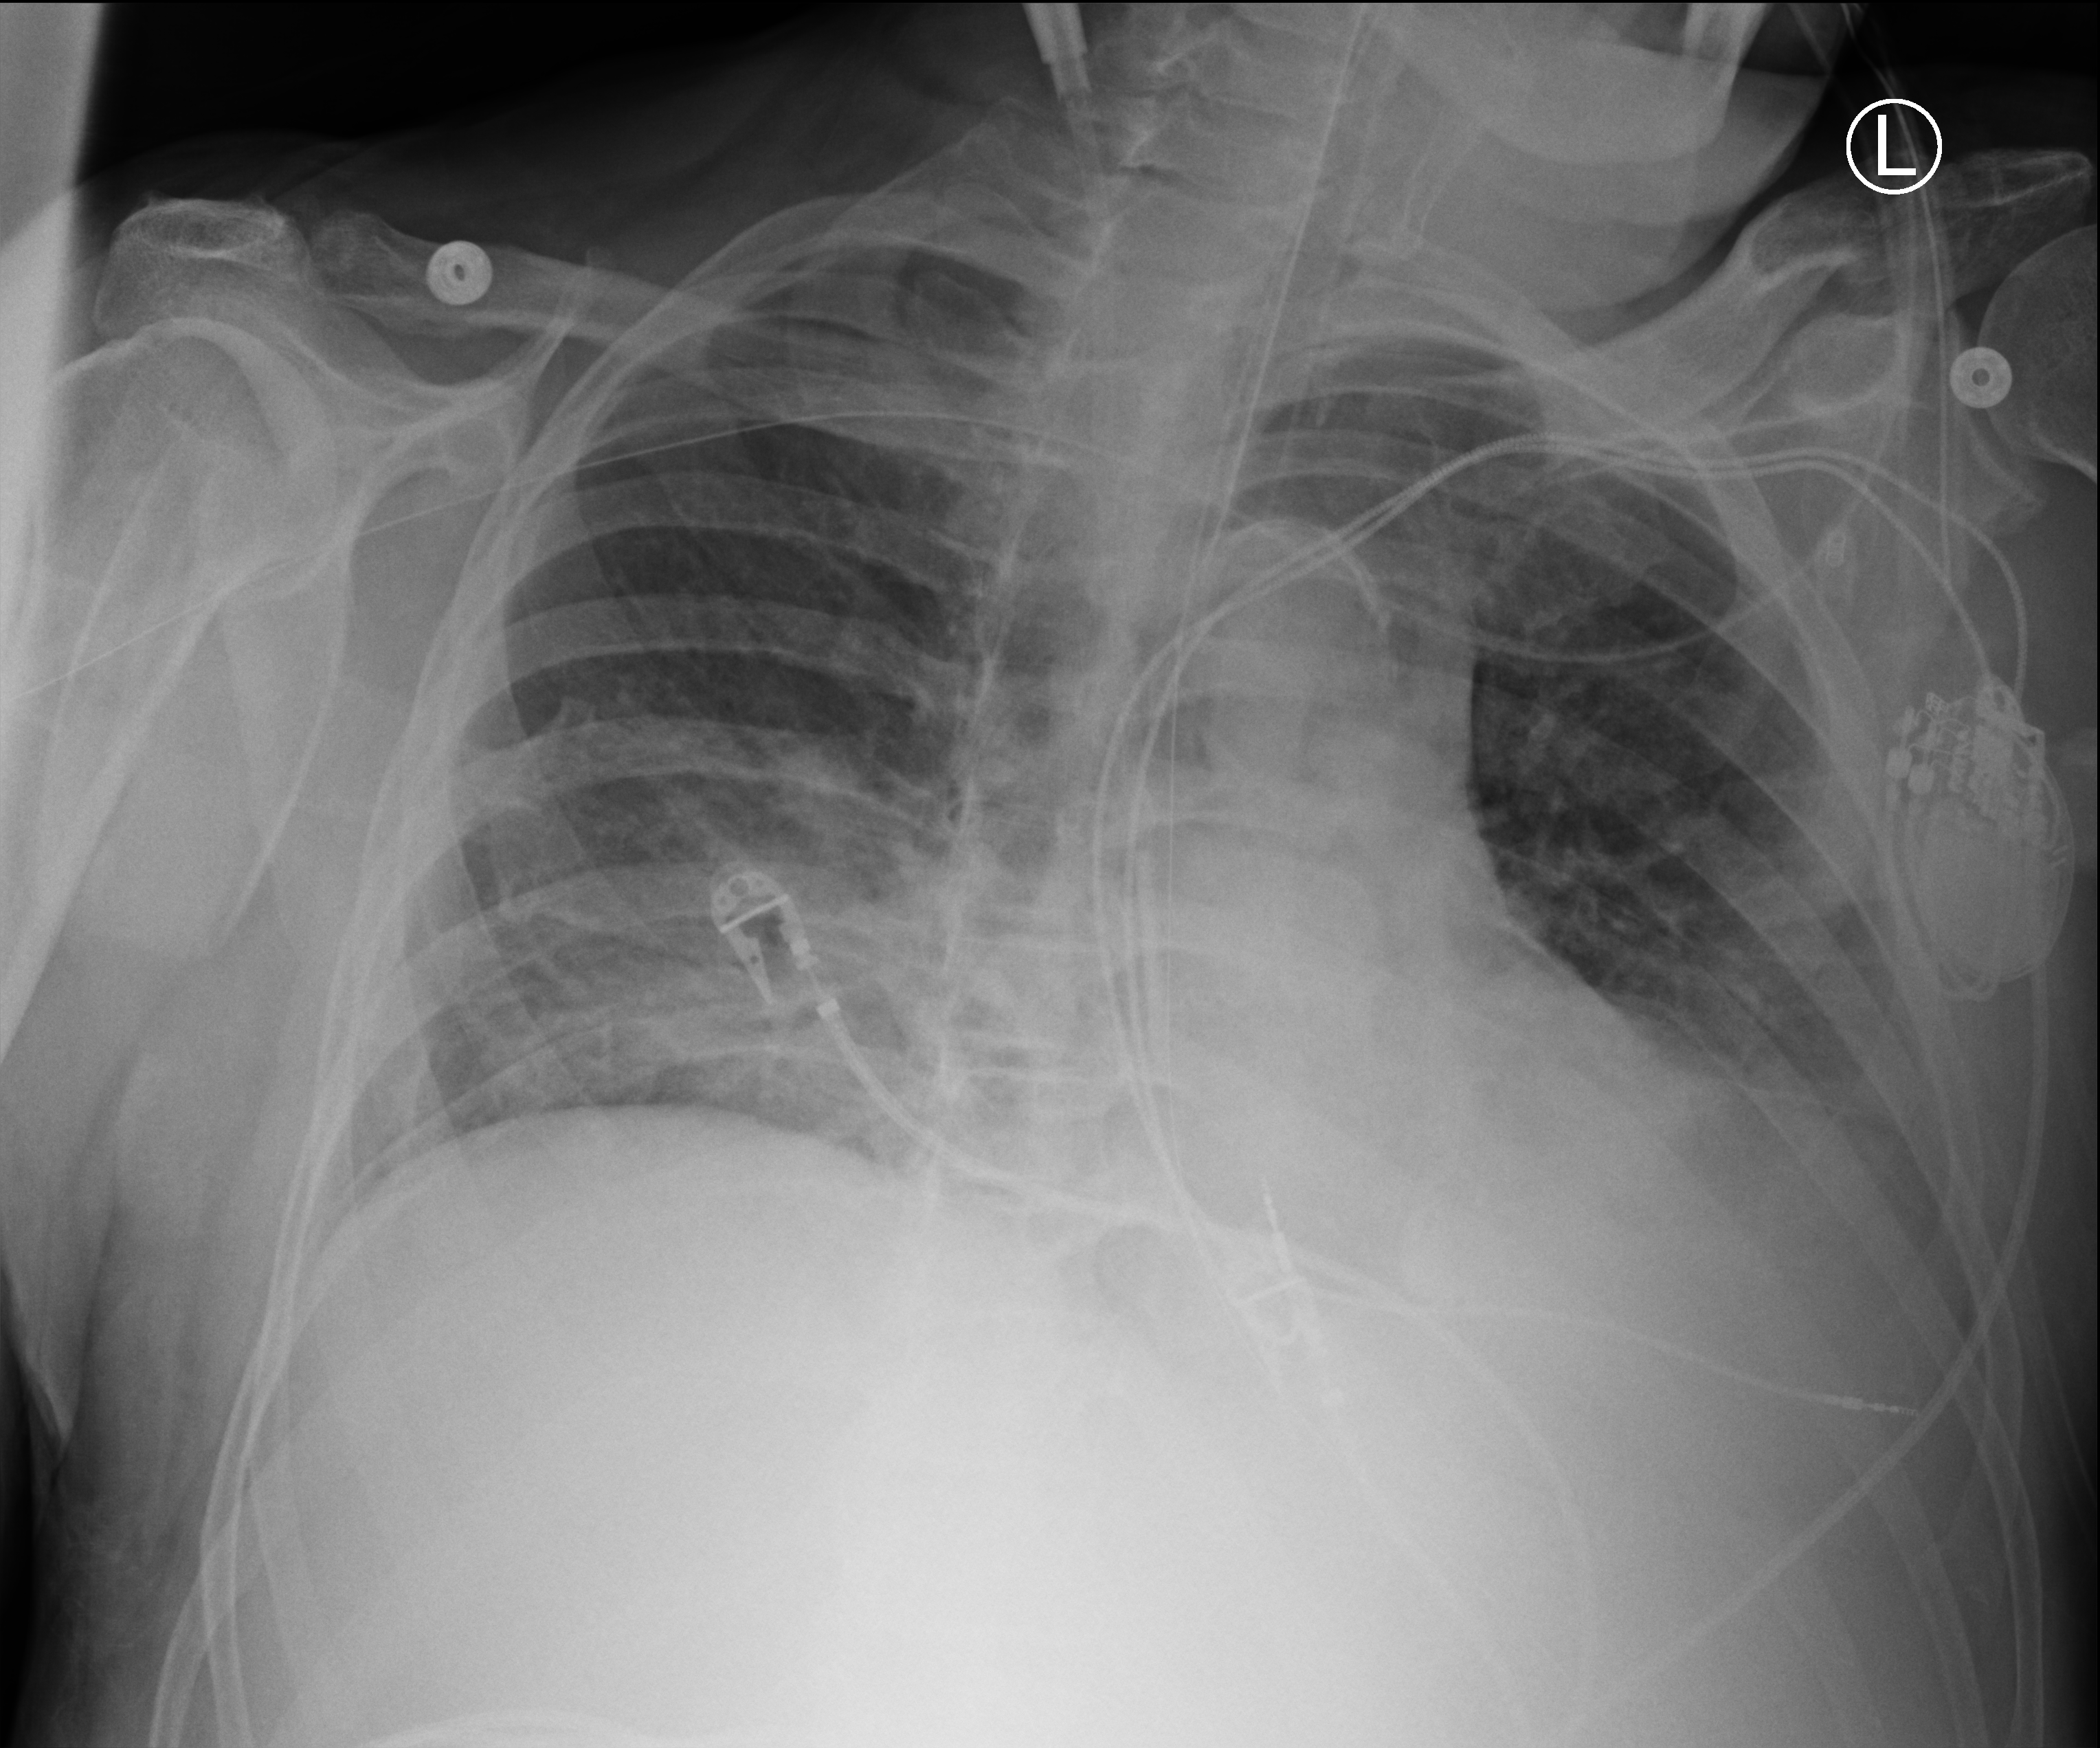
Bedside chest radiograph (computed radiography); anteroposterior (AP) projection. Patient hospitalised with COVID-19; male, aged 60–74 years.
Hospital-stay facts (about this admission, not read from this image; timing relative to this image not recorded): length of hospital stay: 41 days.